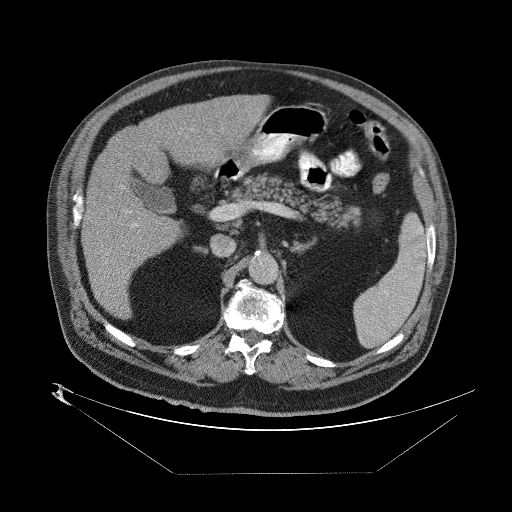
Contrast-enhanced abdominal CT (liver protocol), one axial slice; reconstruction kernel STANDARD; 140 kVp; one of 2 acquisitions stored at this slice position; soft-tissue window (W 400 / L 40 HU); 512 × 512 image matrix, field of view 480 × 480 mm. From the clinical record (not read from this slice): diagnosis: hepatocellular carcinoma (patient treated with transarterial chemoembolisation; whether this scan precedes or follows treatment is not stated here); TNM stage (as recorded): Stage-II; Child-Pugh class: B; tumour nodularity: multinodular; tumour size: 4 cm.
Structures marked on this image (semi-automatic segmentation, software-assisted and operator-edited):
- abdominal aorta: bounding box [x1, y1, x2, y2] px = [249, 255, 276, 282]
- liver parenchyma outside the tumour (the mass and vessels are separate outlines, so this box may not span the whole liver): [82, 92, 267, 320]
- liver vessels: [110, 120, 224, 270]